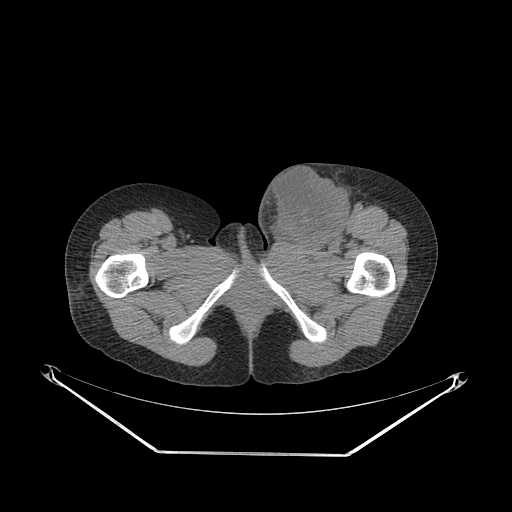
CT of an extremity soft-tissue mass (from a PET/CT study), one axial slice. Position 55 of 267 along the scan axis. 140 kVp. Soft-tissue window (W 400 / L 40 HU). 3.75 mm slice thickness. 512 × 512 image matrix, field of view 500 × 500 mm. Female patient. From the clinical record (not read from this slice): histological type: leiomyosarcoma; grade: high; site of the primary tumour: groin.
Structures marked on this image (expert contour drawn on MRI and transferred to this co-registered scan by the dataset authors):
- gross tumour volume including surrounding oedema: bounding box <253,164,366,248> (left, top, right, bottom; pixels)
- gross tumour volume (mass): <267,167,348,245>